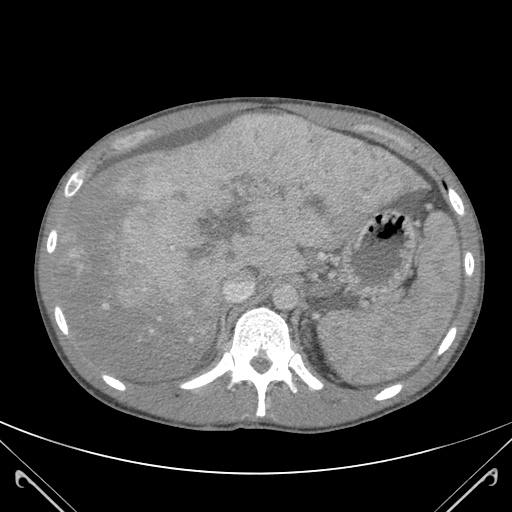
Contrast-enhanced abdominal CT (liver protocol), one axial slice. Slice 85 of 118 in the series (ordered by position). 120 kVp. Soft-tissue window (W 400 / L 40 HU). 512 × 512 image matrix, field of view 380 × 380 mm. Case-level facts recorded for this patient, not image findings: diagnosis: hepatocellular carcinoma (patient treated with transarterial chemoembolisation; whether this scan precedes or follows treatment is not stated here); TNM stage (as recorded): Stage-IIIB; Child-Pugh class: A.
Annotated regions visible in this slice (semi-automatic segmentation, software-assisted and operator-edited):
- abdominal aorta: bounding box [x1, y1, x2, y2] px = [272, 284, 299, 309]
- liver parenchyma outside the tumour (the mass and vessels are separate outlines, so this box may not span the whole liver): [60, 118, 422, 378]
- mass: [95, 121, 412, 327]
- liver vessels: [70, 118, 303, 341]